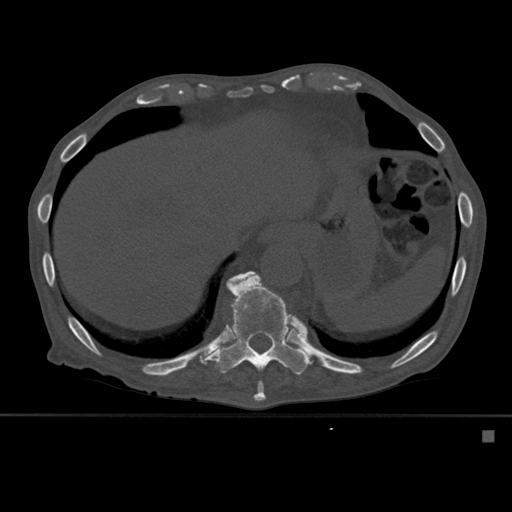
CT including the spine, one axial slice; slice 300 of 527 in the series (ordered by position); bone window (W 1800 / L 400 HU); 1.5 mm slice thickness; 512 × 512 image matrix, field of view 373 × 373 mm. Patient: male, 78 years. Case-level facts recorded for this patient, not image findings: primary cancer: prostate.
Annotated regions visible in this slice (semi-automatically segmented with operator editing):
- T10 vertebra: bounding box <234,272,266,401> (left, top, right, bottom; pixels)
- T11 vertebra: <202,271,313,375>